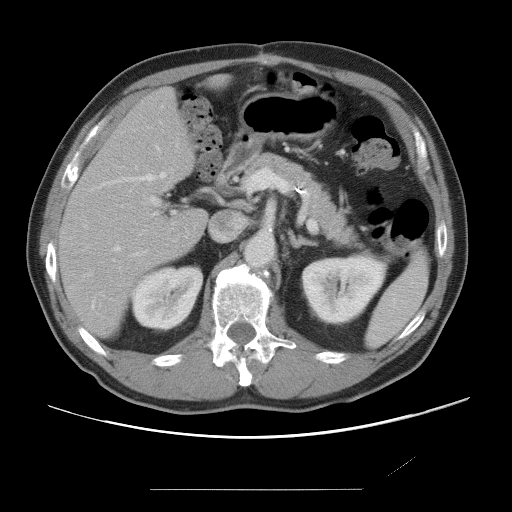
Contrast-enhanced abdominal CT, one axial slice; position 39 of 87 along the scan axis; soft-tissue window (W 400 / L 40 HU); 5 mm slice thickness; 512 × 512 image matrix, field of view 406 × 406 mm. Male patient, age 74 years. From the clinical record (not read from this slice): diagnosis: colorectal cancer liver metastases, imaged before liver resection; multiple liver metastases: yes; largest metastasis: 1.1 cm; disease in both lobes: no.
Structures marked on this image (outlined manually by an expert reader):
- hepatic veins: bounding box (x1, y1, x2, y2) in pixels: (92, 147, 166, 308)
- liver: (61, 89, 207, 335)
- planned liver remnant (the part of the liver to remain after resection): (61, 89, 206, 335)
- portal vein (with intrahepatic branches): (135, 167, 274, 254)